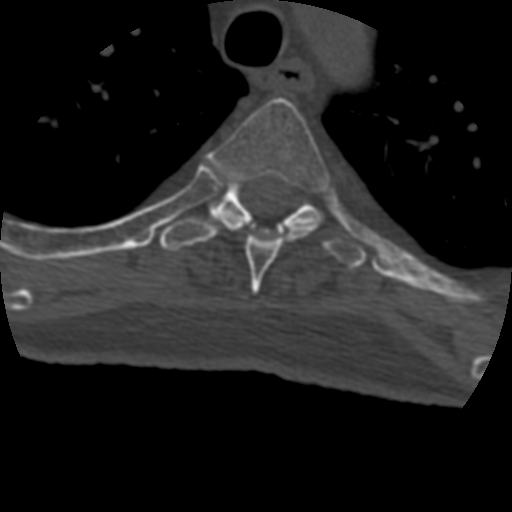
CT including the spine, one axial slice; position 330 of 399 along the scan axis; reconstruction kernel STANDARD; bone window (W 1800 / L 400 HU); 1.25 mm slice thickness; 512 × 512 image matrix. Patient age 69 years. Case-level facts recorded for this patient, not image findings: primary cancer: prostate.
Structures marked on this image (semi-automatic segmentation, software-assisted and operator-edited):
- T4 vertebra: bounding box <206,98,330,294> (left, top, right, bottom; pixels)
- T5 vertebra: <160,181,368,269>